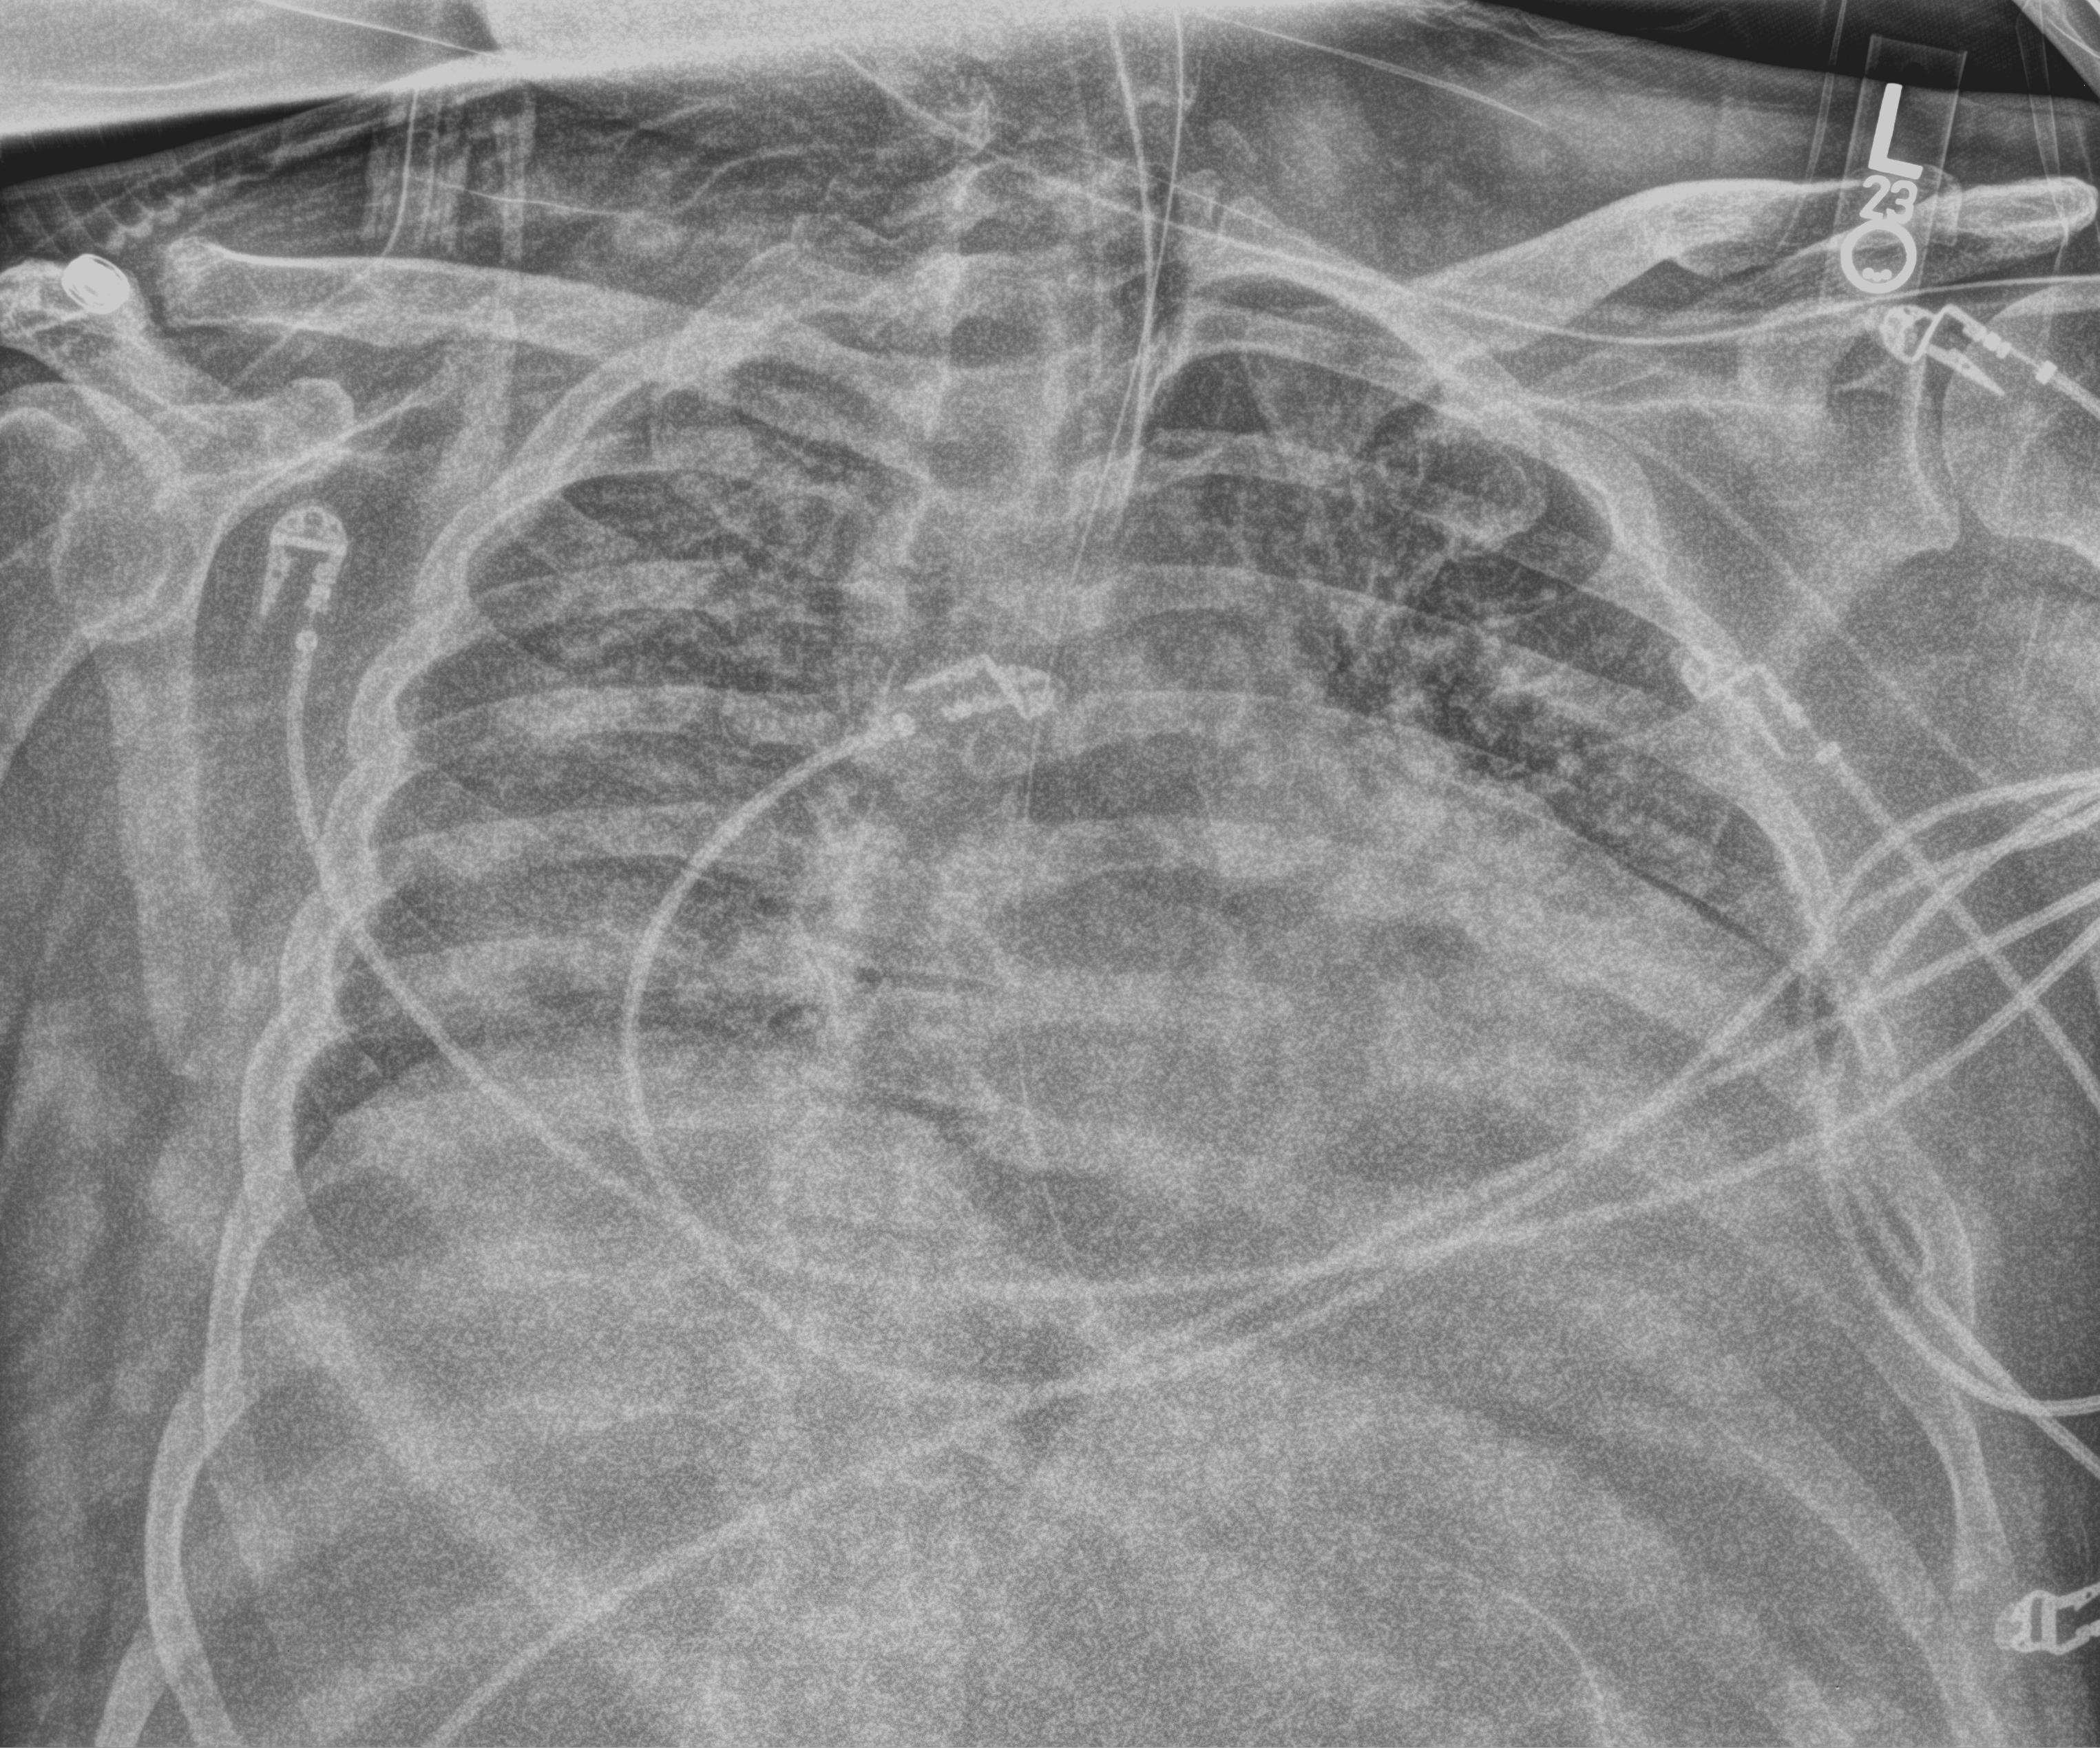
Chest X-ray (portable); anteroposterior (AP) projection. Patient hospitalised with COVID-19; male, aged 18–59 years.
From the hospital-stay record, not from the radiograph (when in the stay this image was taken is not recorded): mechanically ventilated during this hospital stay: yes; COPD (admission record): no.